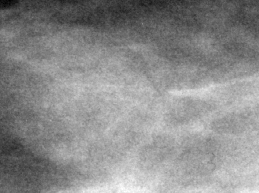
Cropped region of a digitized screen-film mammogram centred on a radiologist-marked abnormality, right breast, CC view.
Mass, shape oval, margins circumscribed / obscured; BI-RADS assessment category 4; pathology result (as recorded, not read from the image): benign.